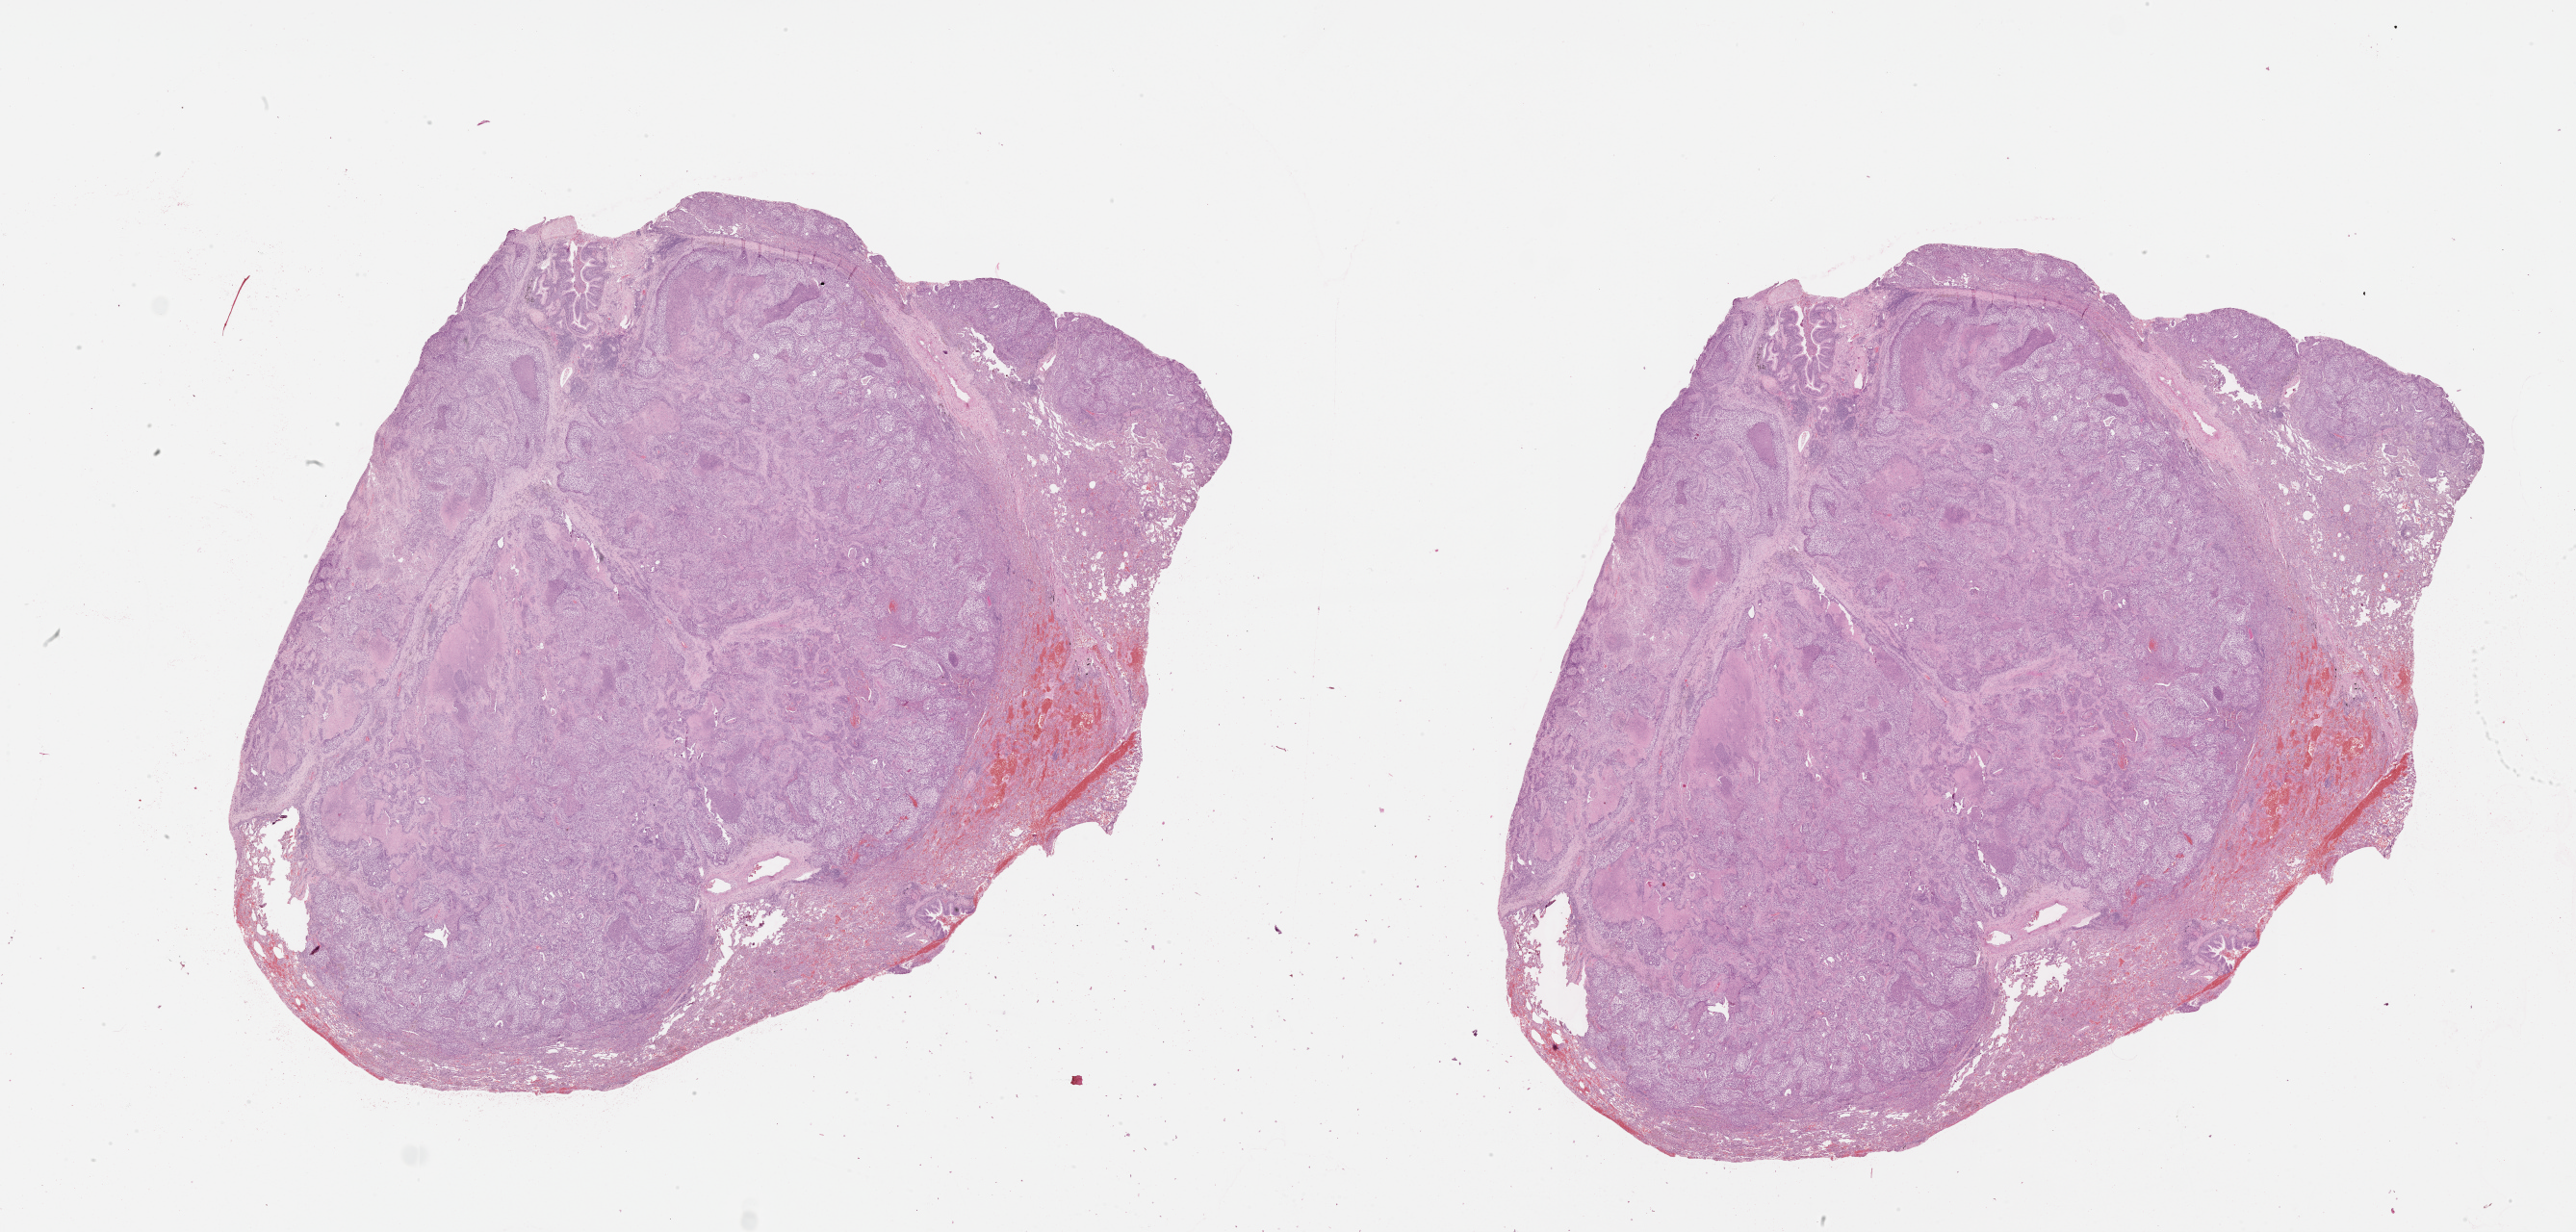
H&E whole-slide image — low-resolution overview of the scanned area, about 43.1 x 20.6 mm (from a 20x scan). Lung, tumour tissue. Patient: male, age 56 years.
Patient diagnosis (cohort enrolment): squamous cell carcinoma (lung).